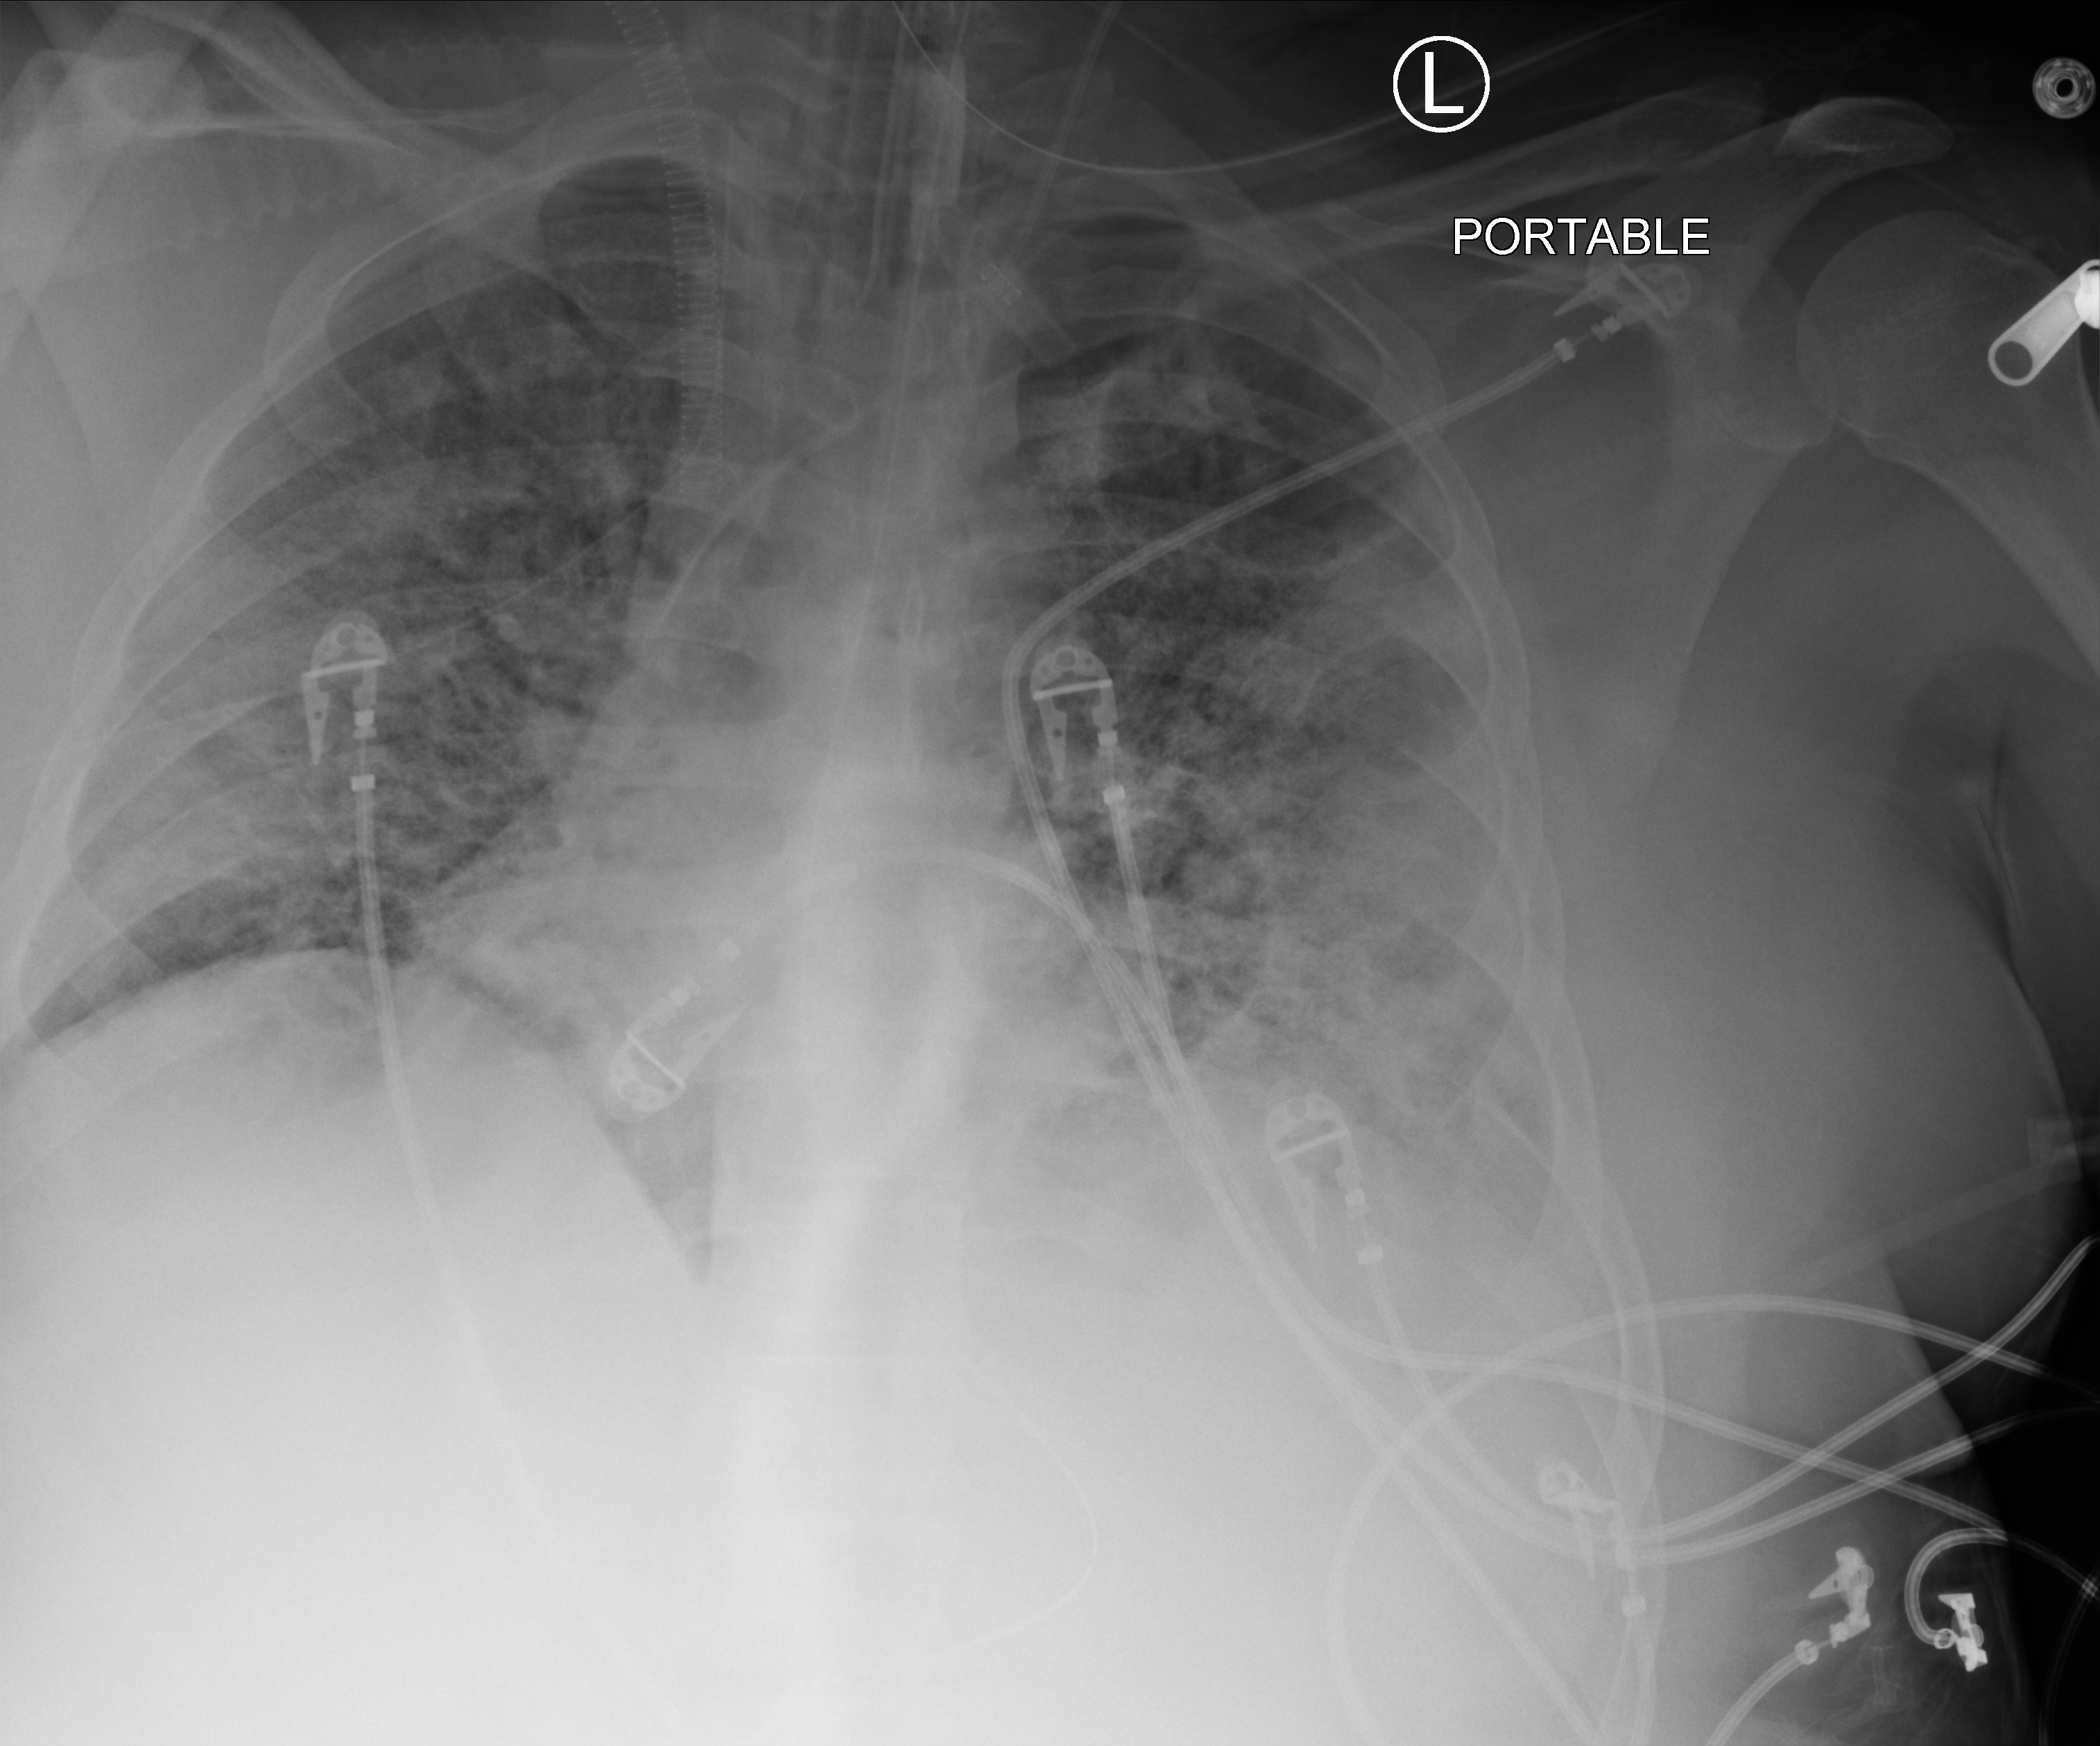
Portable chest radiograph, anteroposterior (AP) projection. Adult patient hospitalised with COVID-19, age 18–59 years.
From the hospital-stay record, not from the radiograph (when in the stay this image was taken is not recorded): mechanically ventilated during this hospital stay: yes.